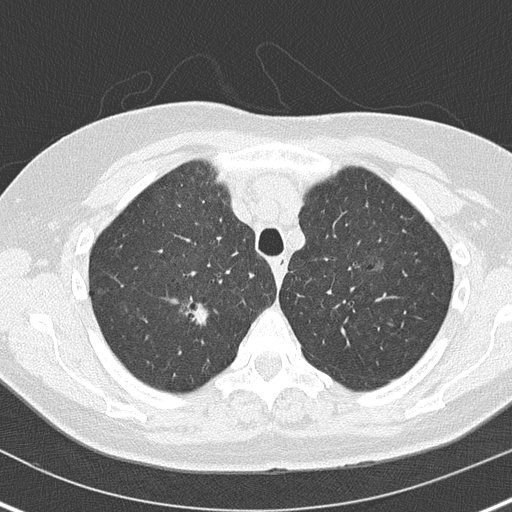
Axial slice from a low-dose chest CT screening exam. First (baseline) screen. Lung window (W 1500 / L -600 HU). 2 mm slice thickness. Slice 37 of 162 in the series. 512 × 512 image matrix, field of view 300 × 300 mm. Female, age 61 years at enrolment. Current smoker at enrolment.
Expert reader's lesion annotation, box from (x=179, y=294) to (x=219, y=329) px. Screening reader's record for this exam (one nodule recorded; not confirmed to be the boxed lesion): non-calcified nodule or mass ≥4 mm, right upper lobe, 8 × 5 mm, smooth margins, soft tissue attenuation. Official screen result: positive, change unspecified: nodule(s) >= 4 mm or enlarging nodule(s), mass(es), or other non-specific abnormalities suspicious for lung cancer. Participant outcome: lung cancer diagnosed 438 days after this screen — adenocarcinoma, NOS, right upper lobe, moderately differentiated (G2), stage IA (AJCC 6th edition), 20 mm at pathology.